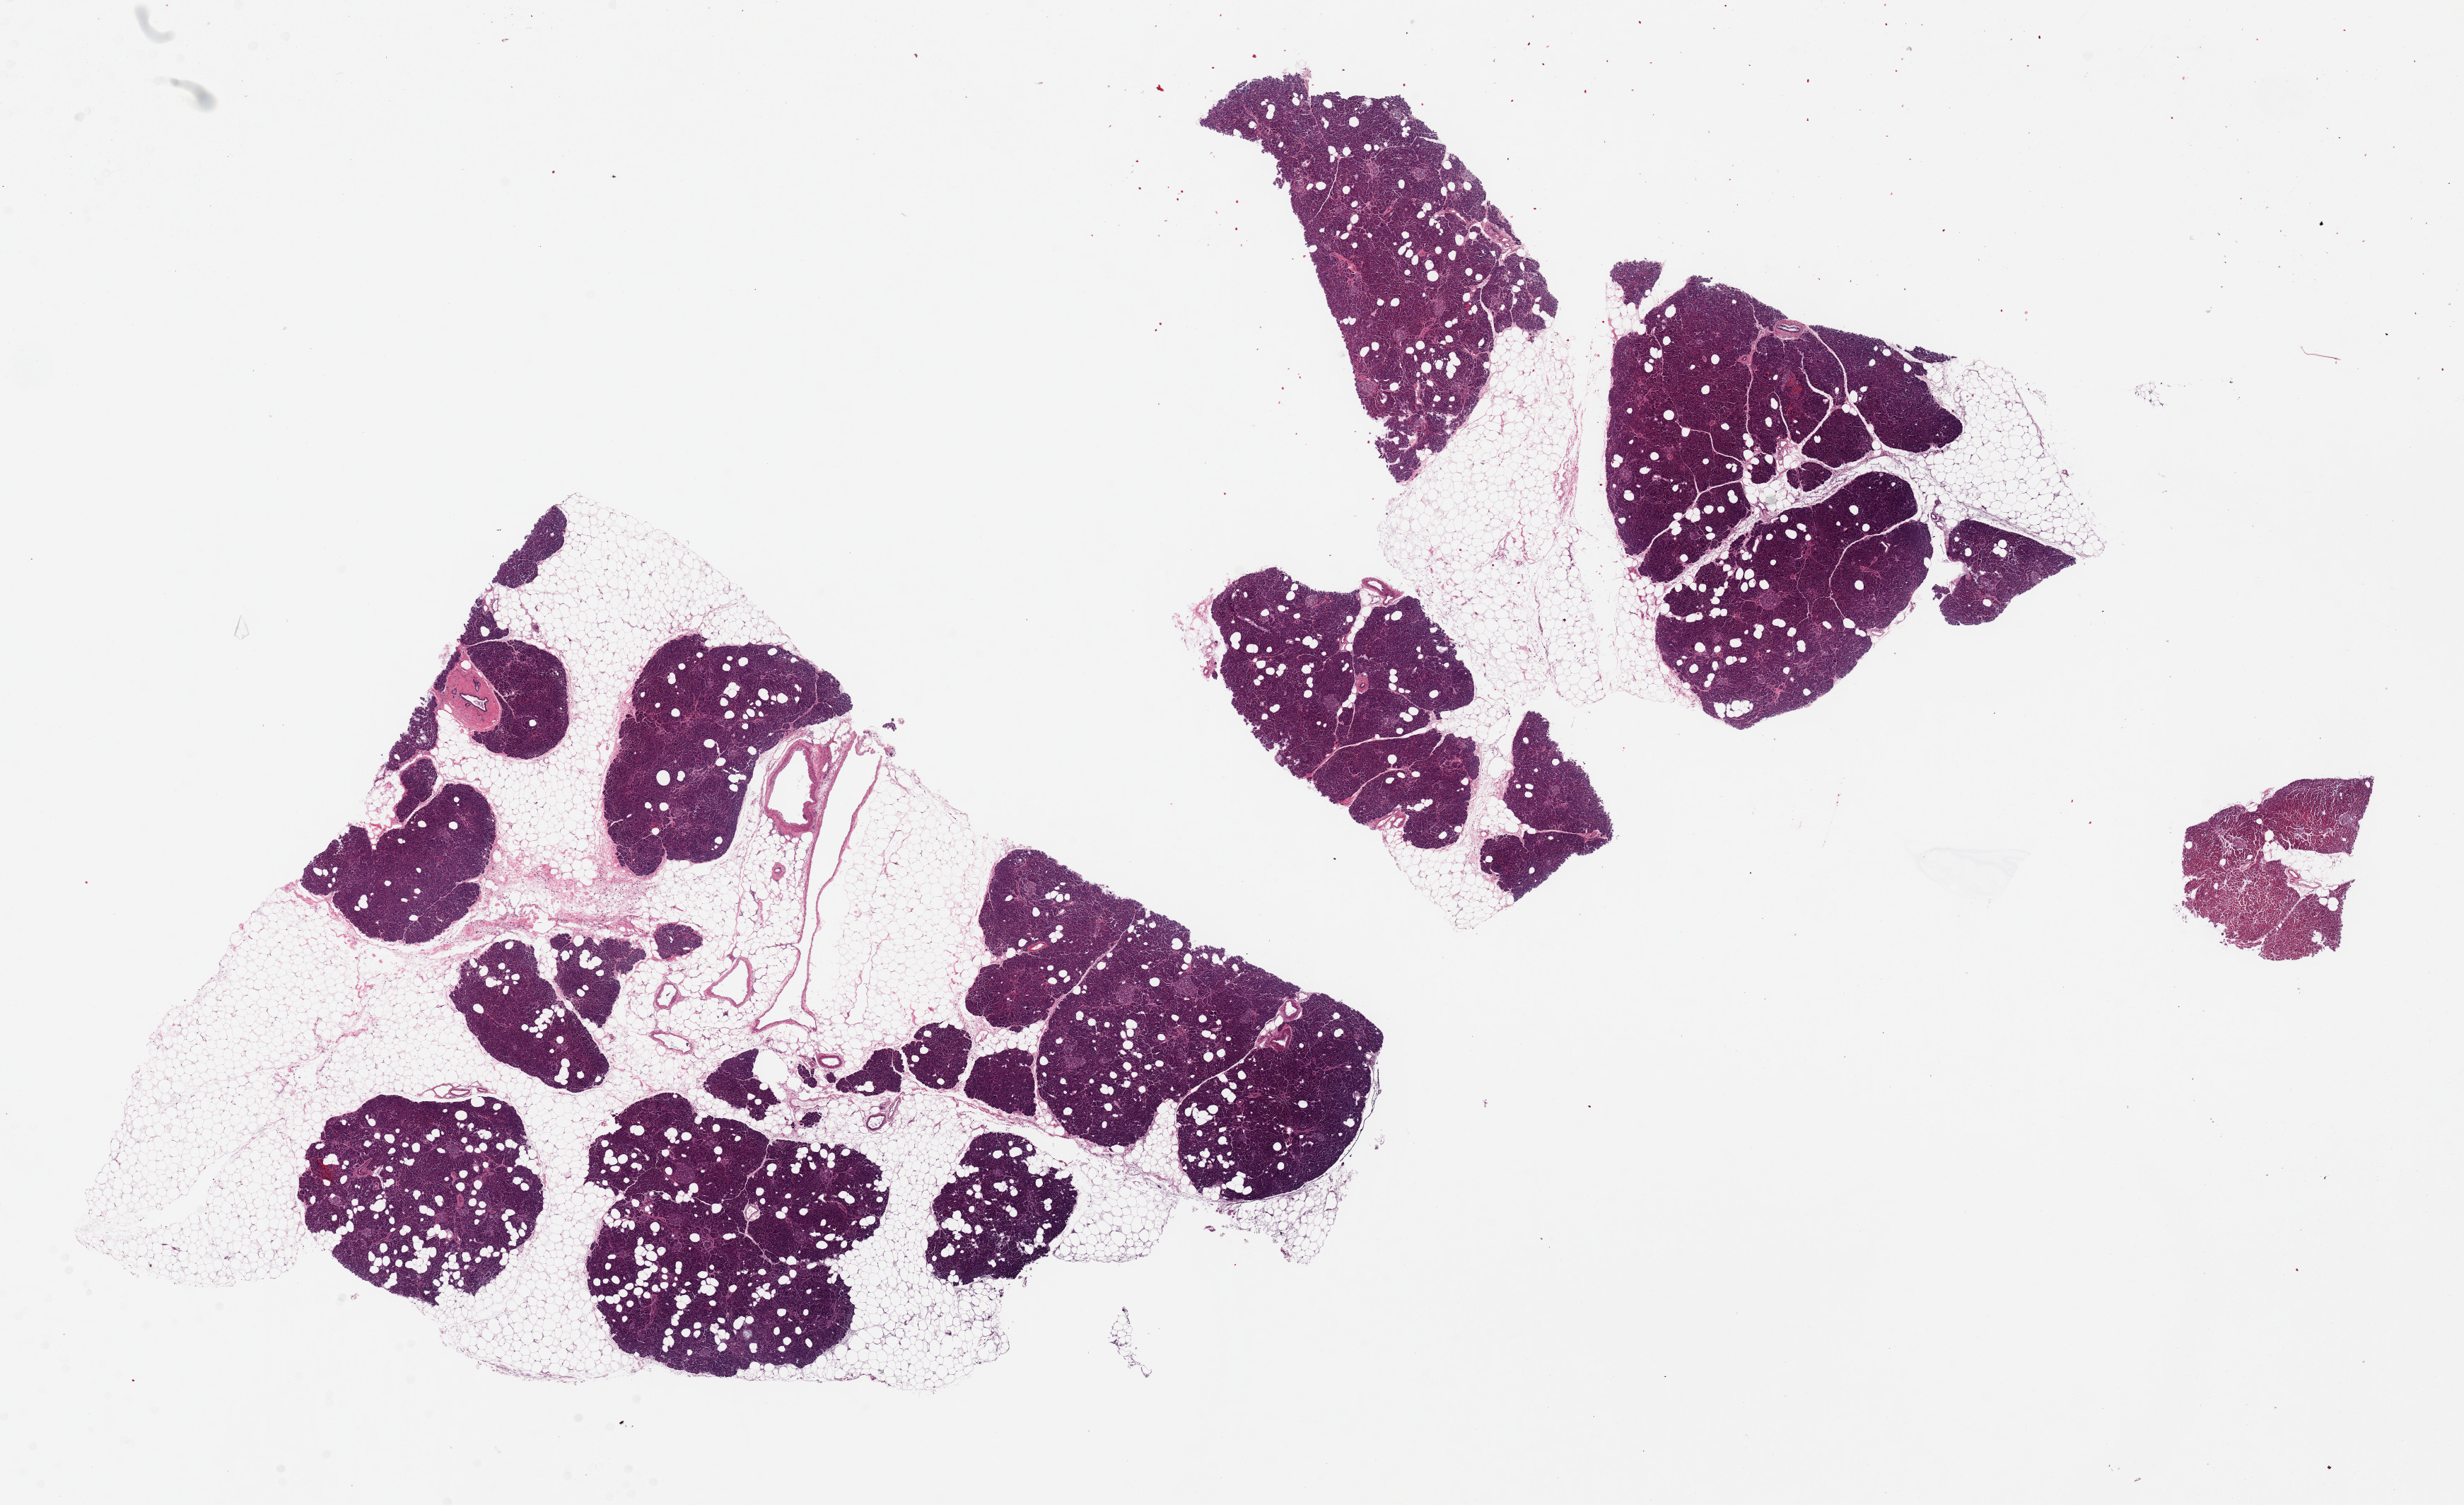
Digitized H&E-stained section — a low-resolution overview of the entire scanned area, about 27.6 x 16.8 mm (acquisition: 20x scan). PAXgene-fixed paraffin-embedded (PFPE) section. Section of pancreas (target tissue). Donor tissue sample.
Pathologist's review note for this sample: 2 pieces and small fragment, larger pieces are ~40--60% adipose tissue.